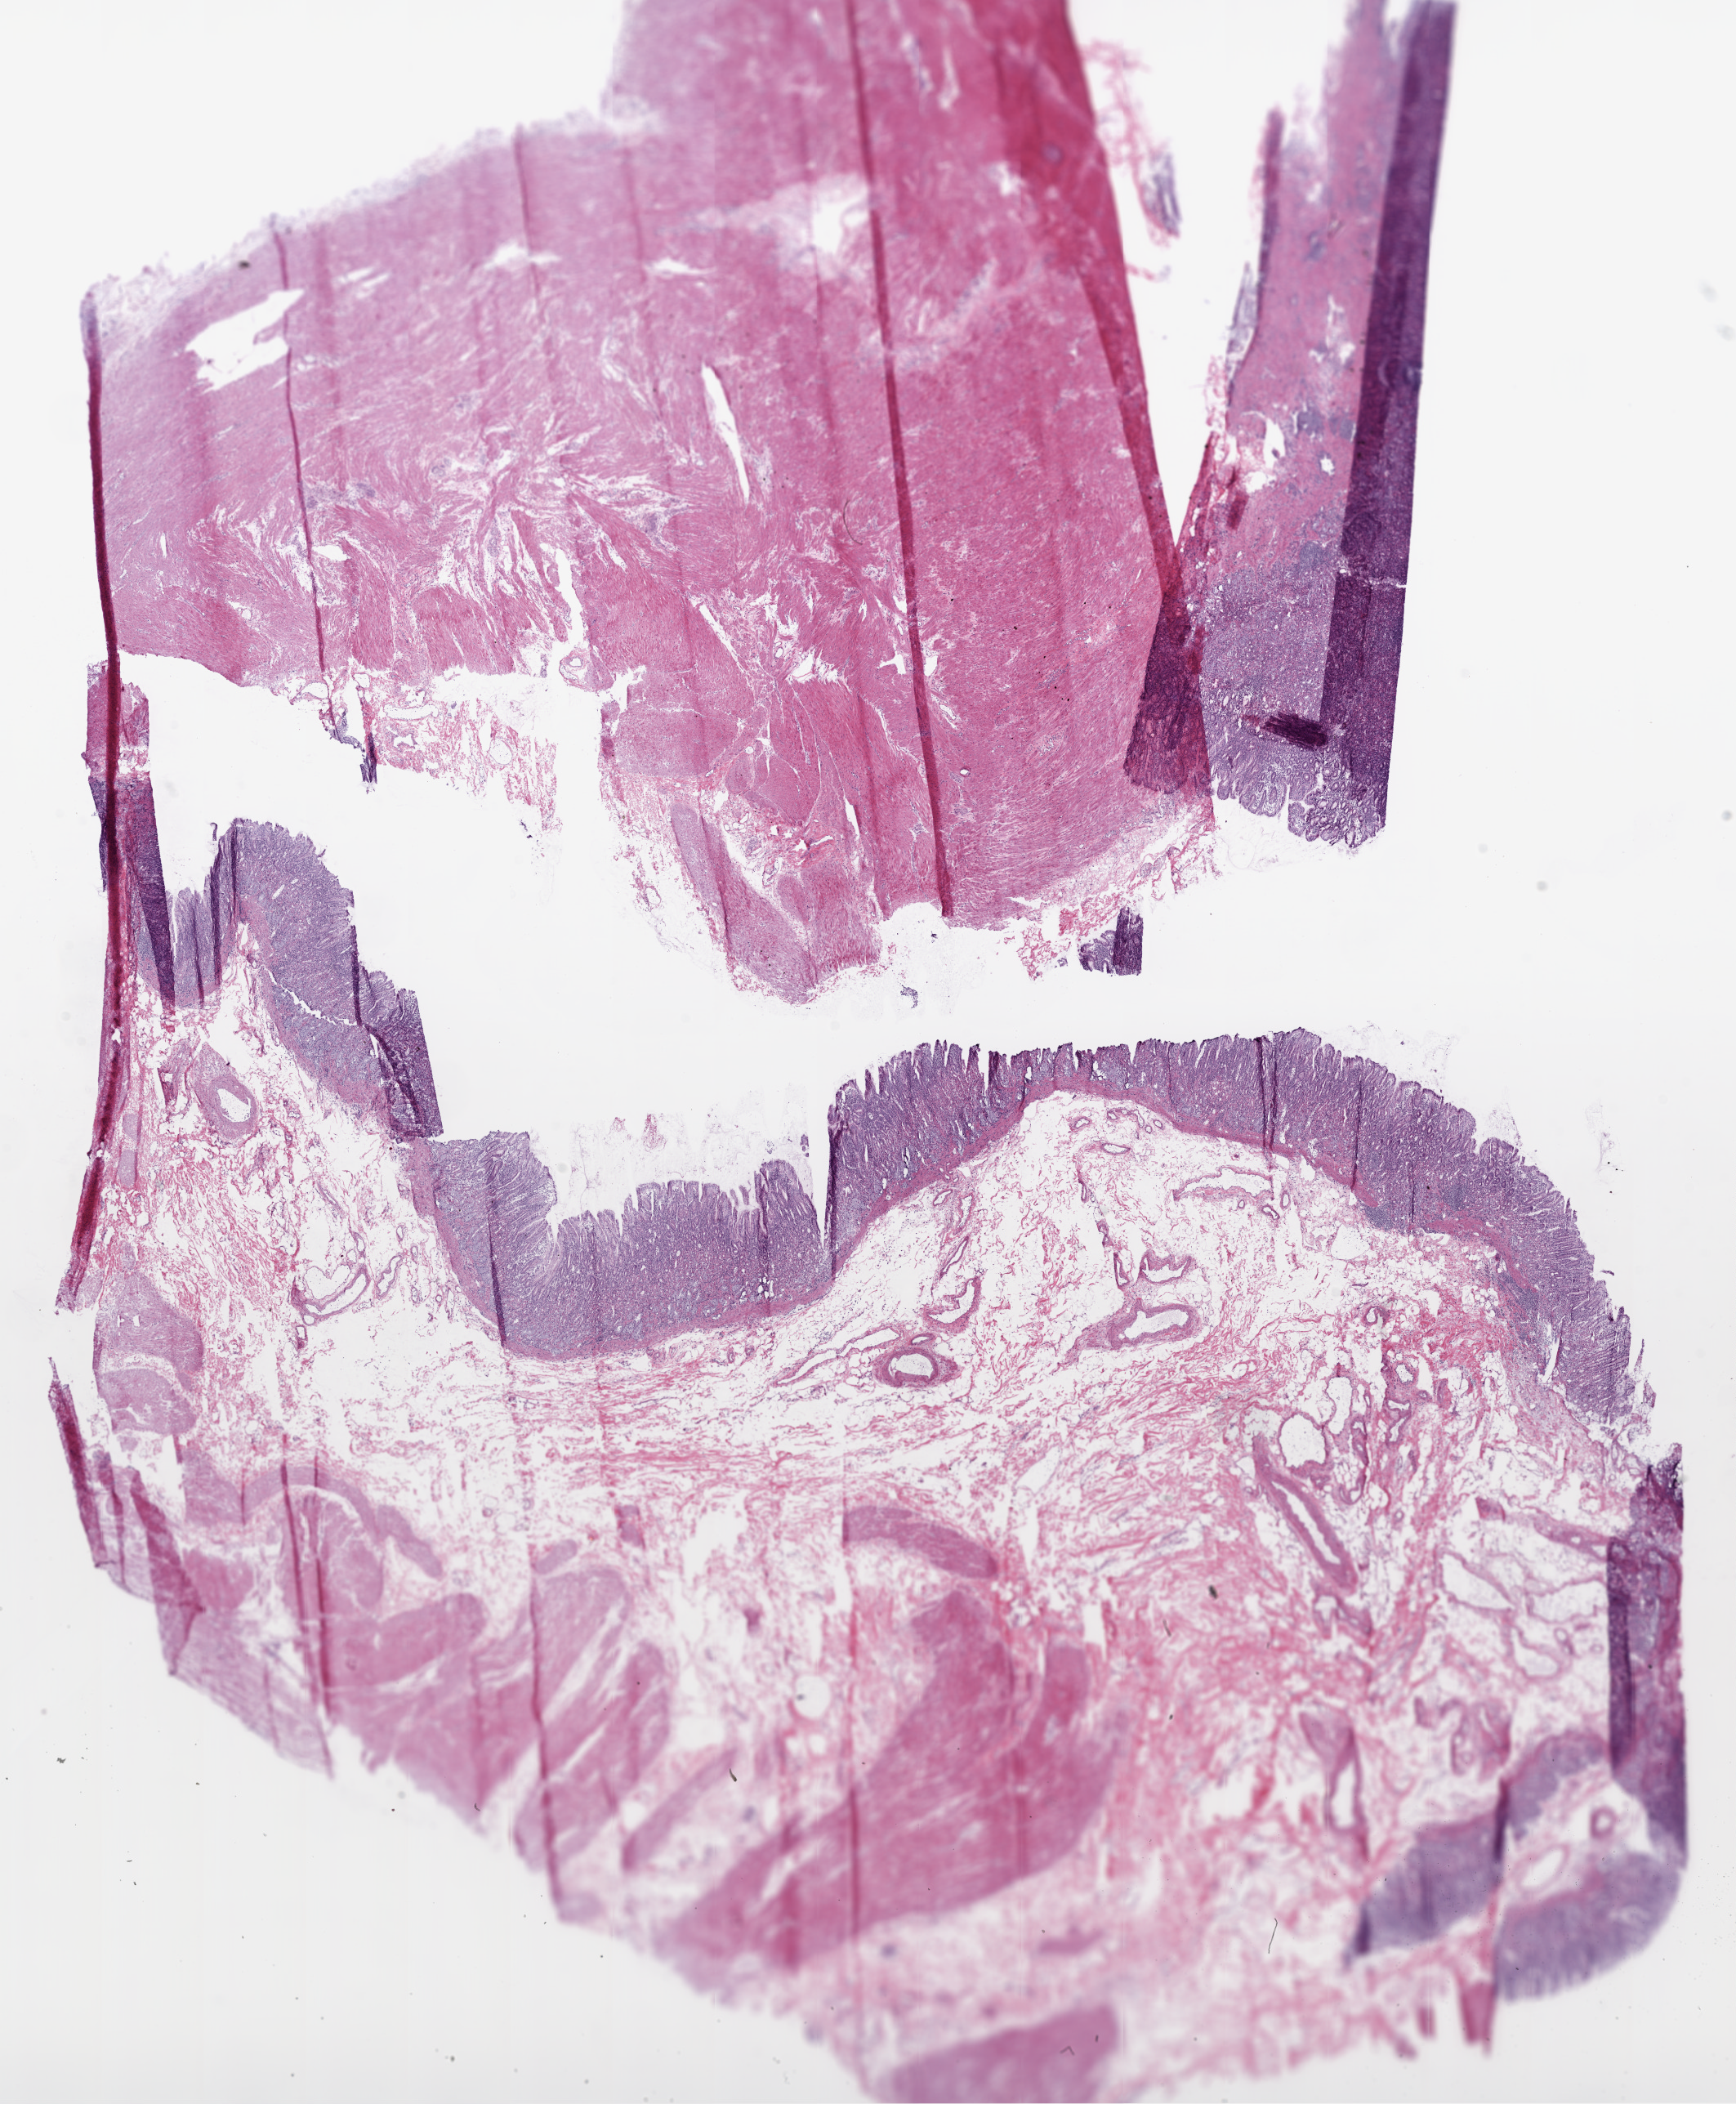
Digitized H&E tissue section (whole slide) — shown as a low-resolution overview of the whole scanned area (about 17.1 x 20.7 mm), frozen section from the top of the tissue portion, solid tissue normal (non-tumour tissue) sample from the stomach. Patient: male, age at initial diagnosis 87 years.
This section: solid tissue normal sample (biorepository sample class). Patient diagnosis: Adenocarcinoma, NOS (gastric antrum).